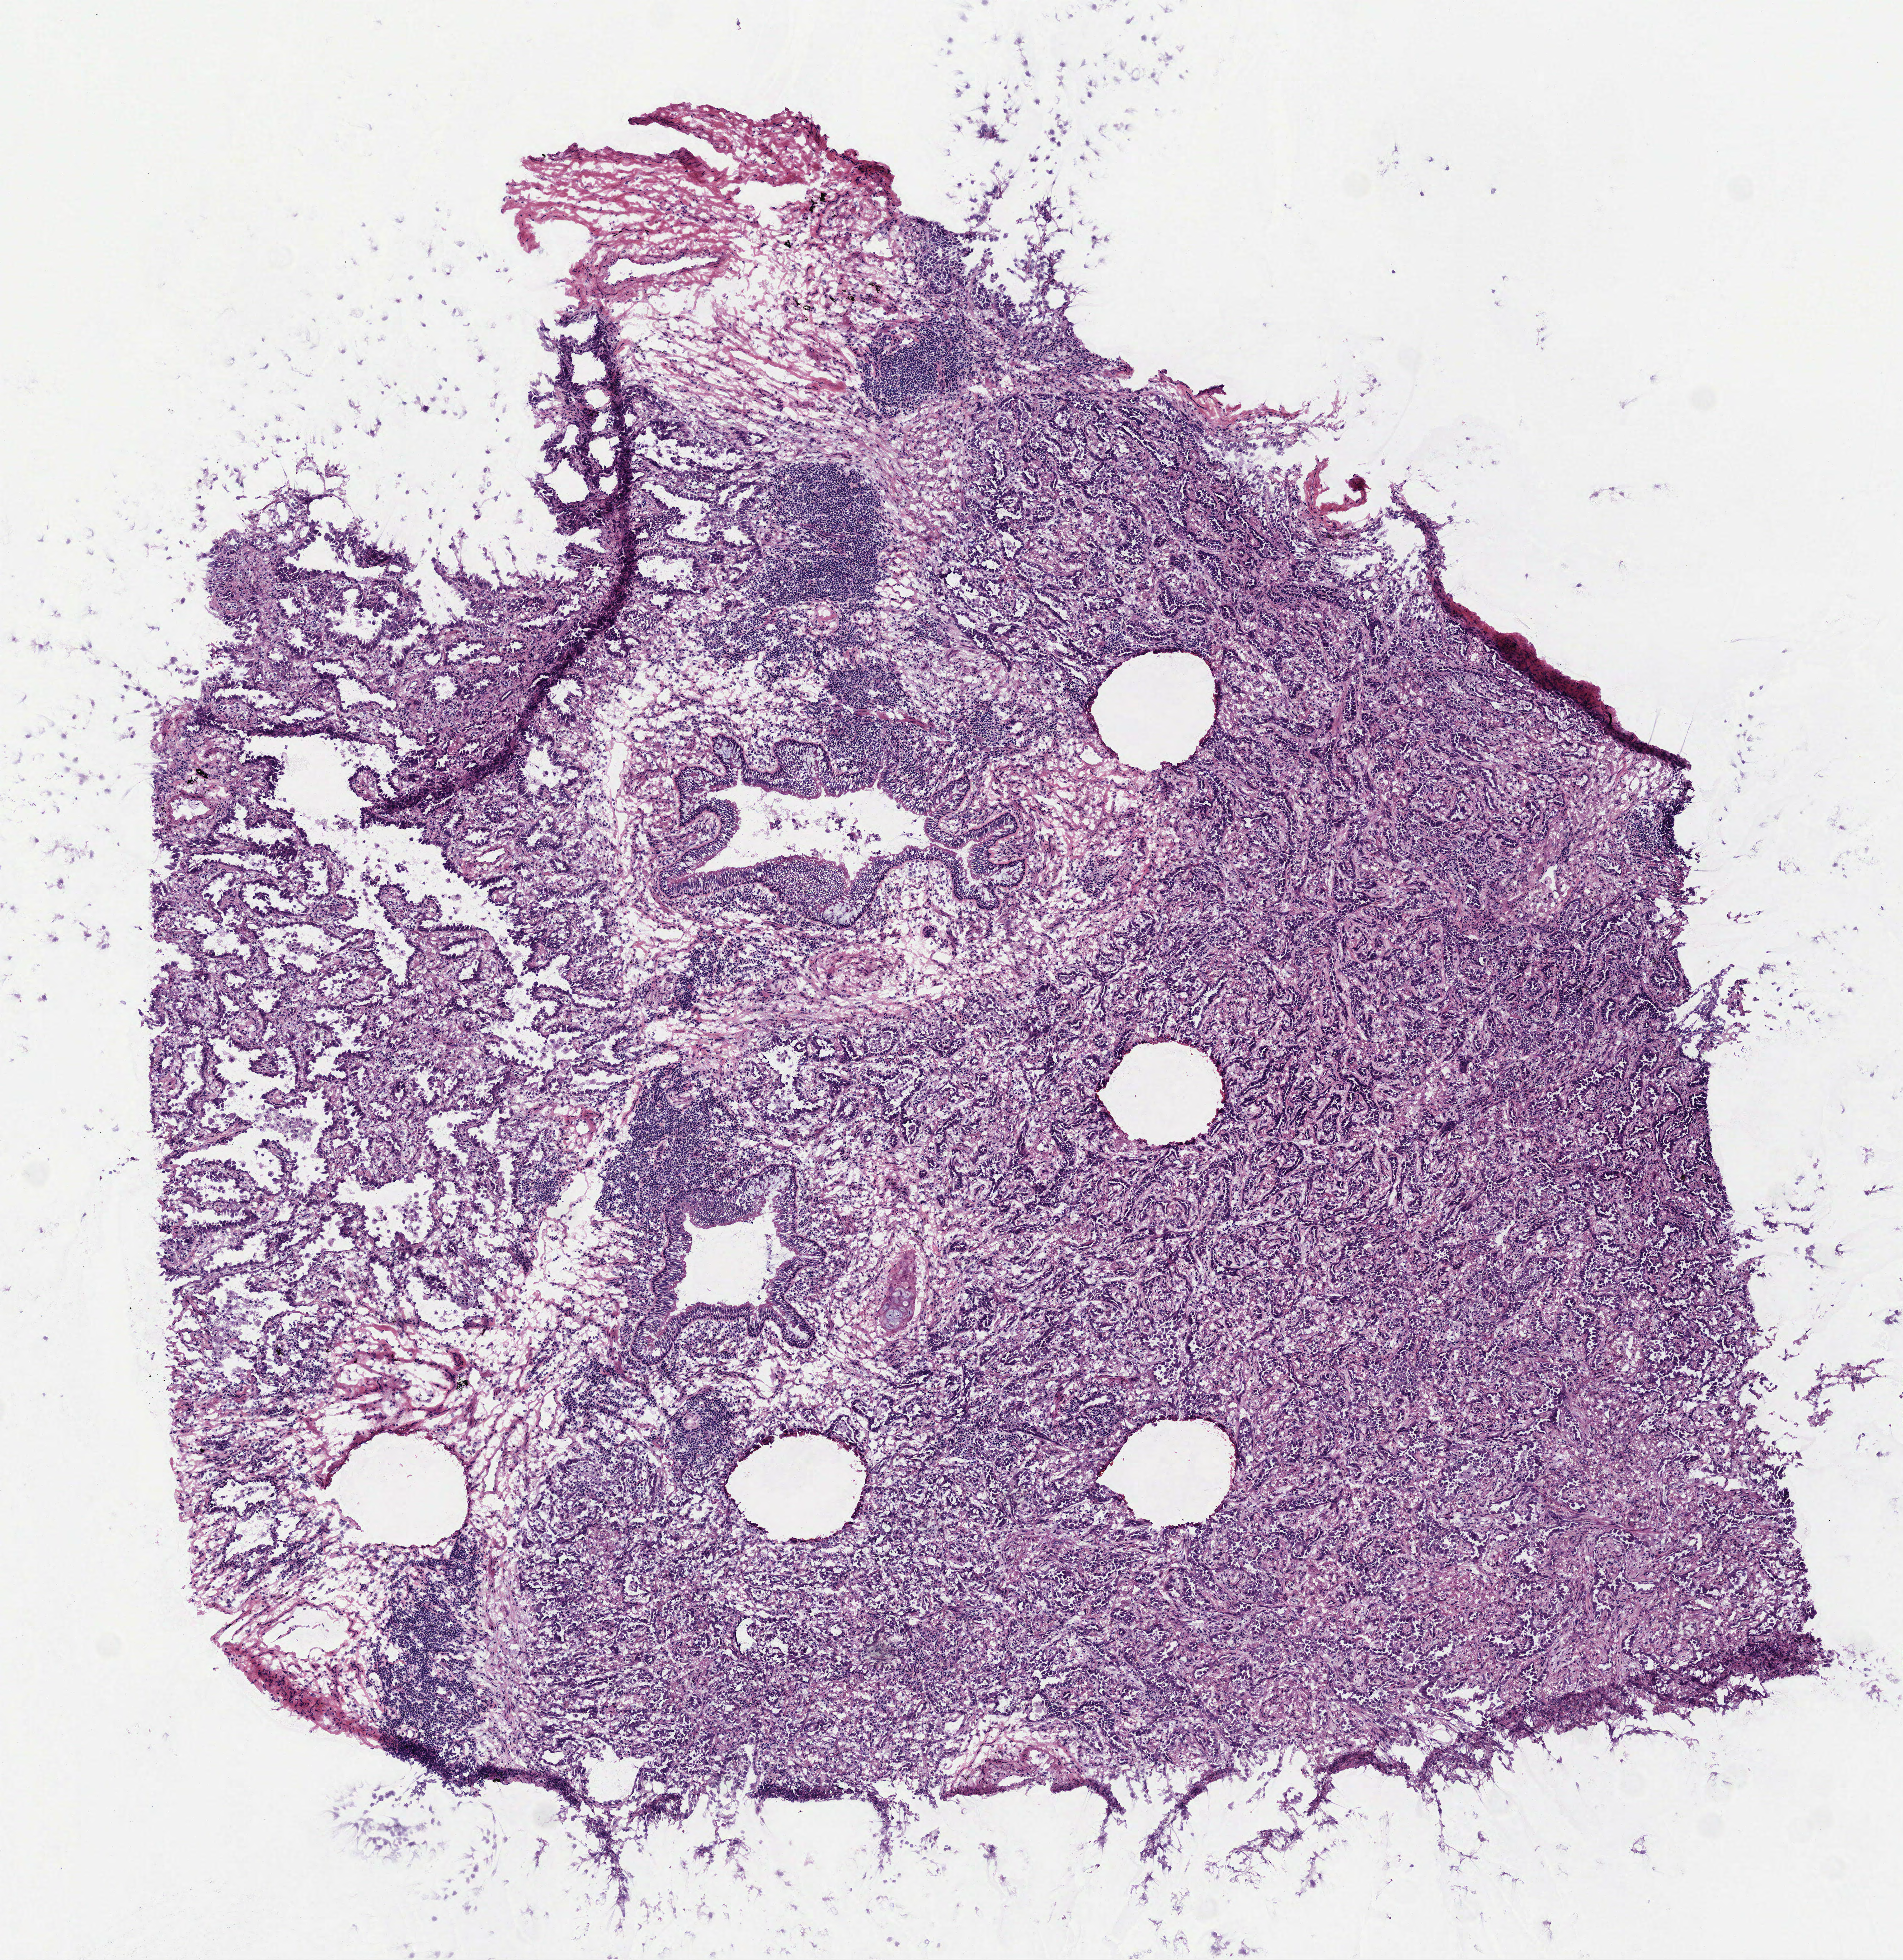
Whole-slide histology image, Hematoxylin and eosin (H&E) stained, shown as a low-resolution overview of the whole scanned area (about 6.0 x 6.2 mm, from a 40x scan). Frozen section from the top of the tissue portion. Sample: primary tumour, lung. Female patient; age at initial diagnosis 72 years. Slide review estimates, as recorded: tumour nuclei 65%, necrosis 0%.
- pathologic diagnosis: Adenocarcinoma, NOS
- laterality: right
- AJCC pathologic stage: IA (7th edition)